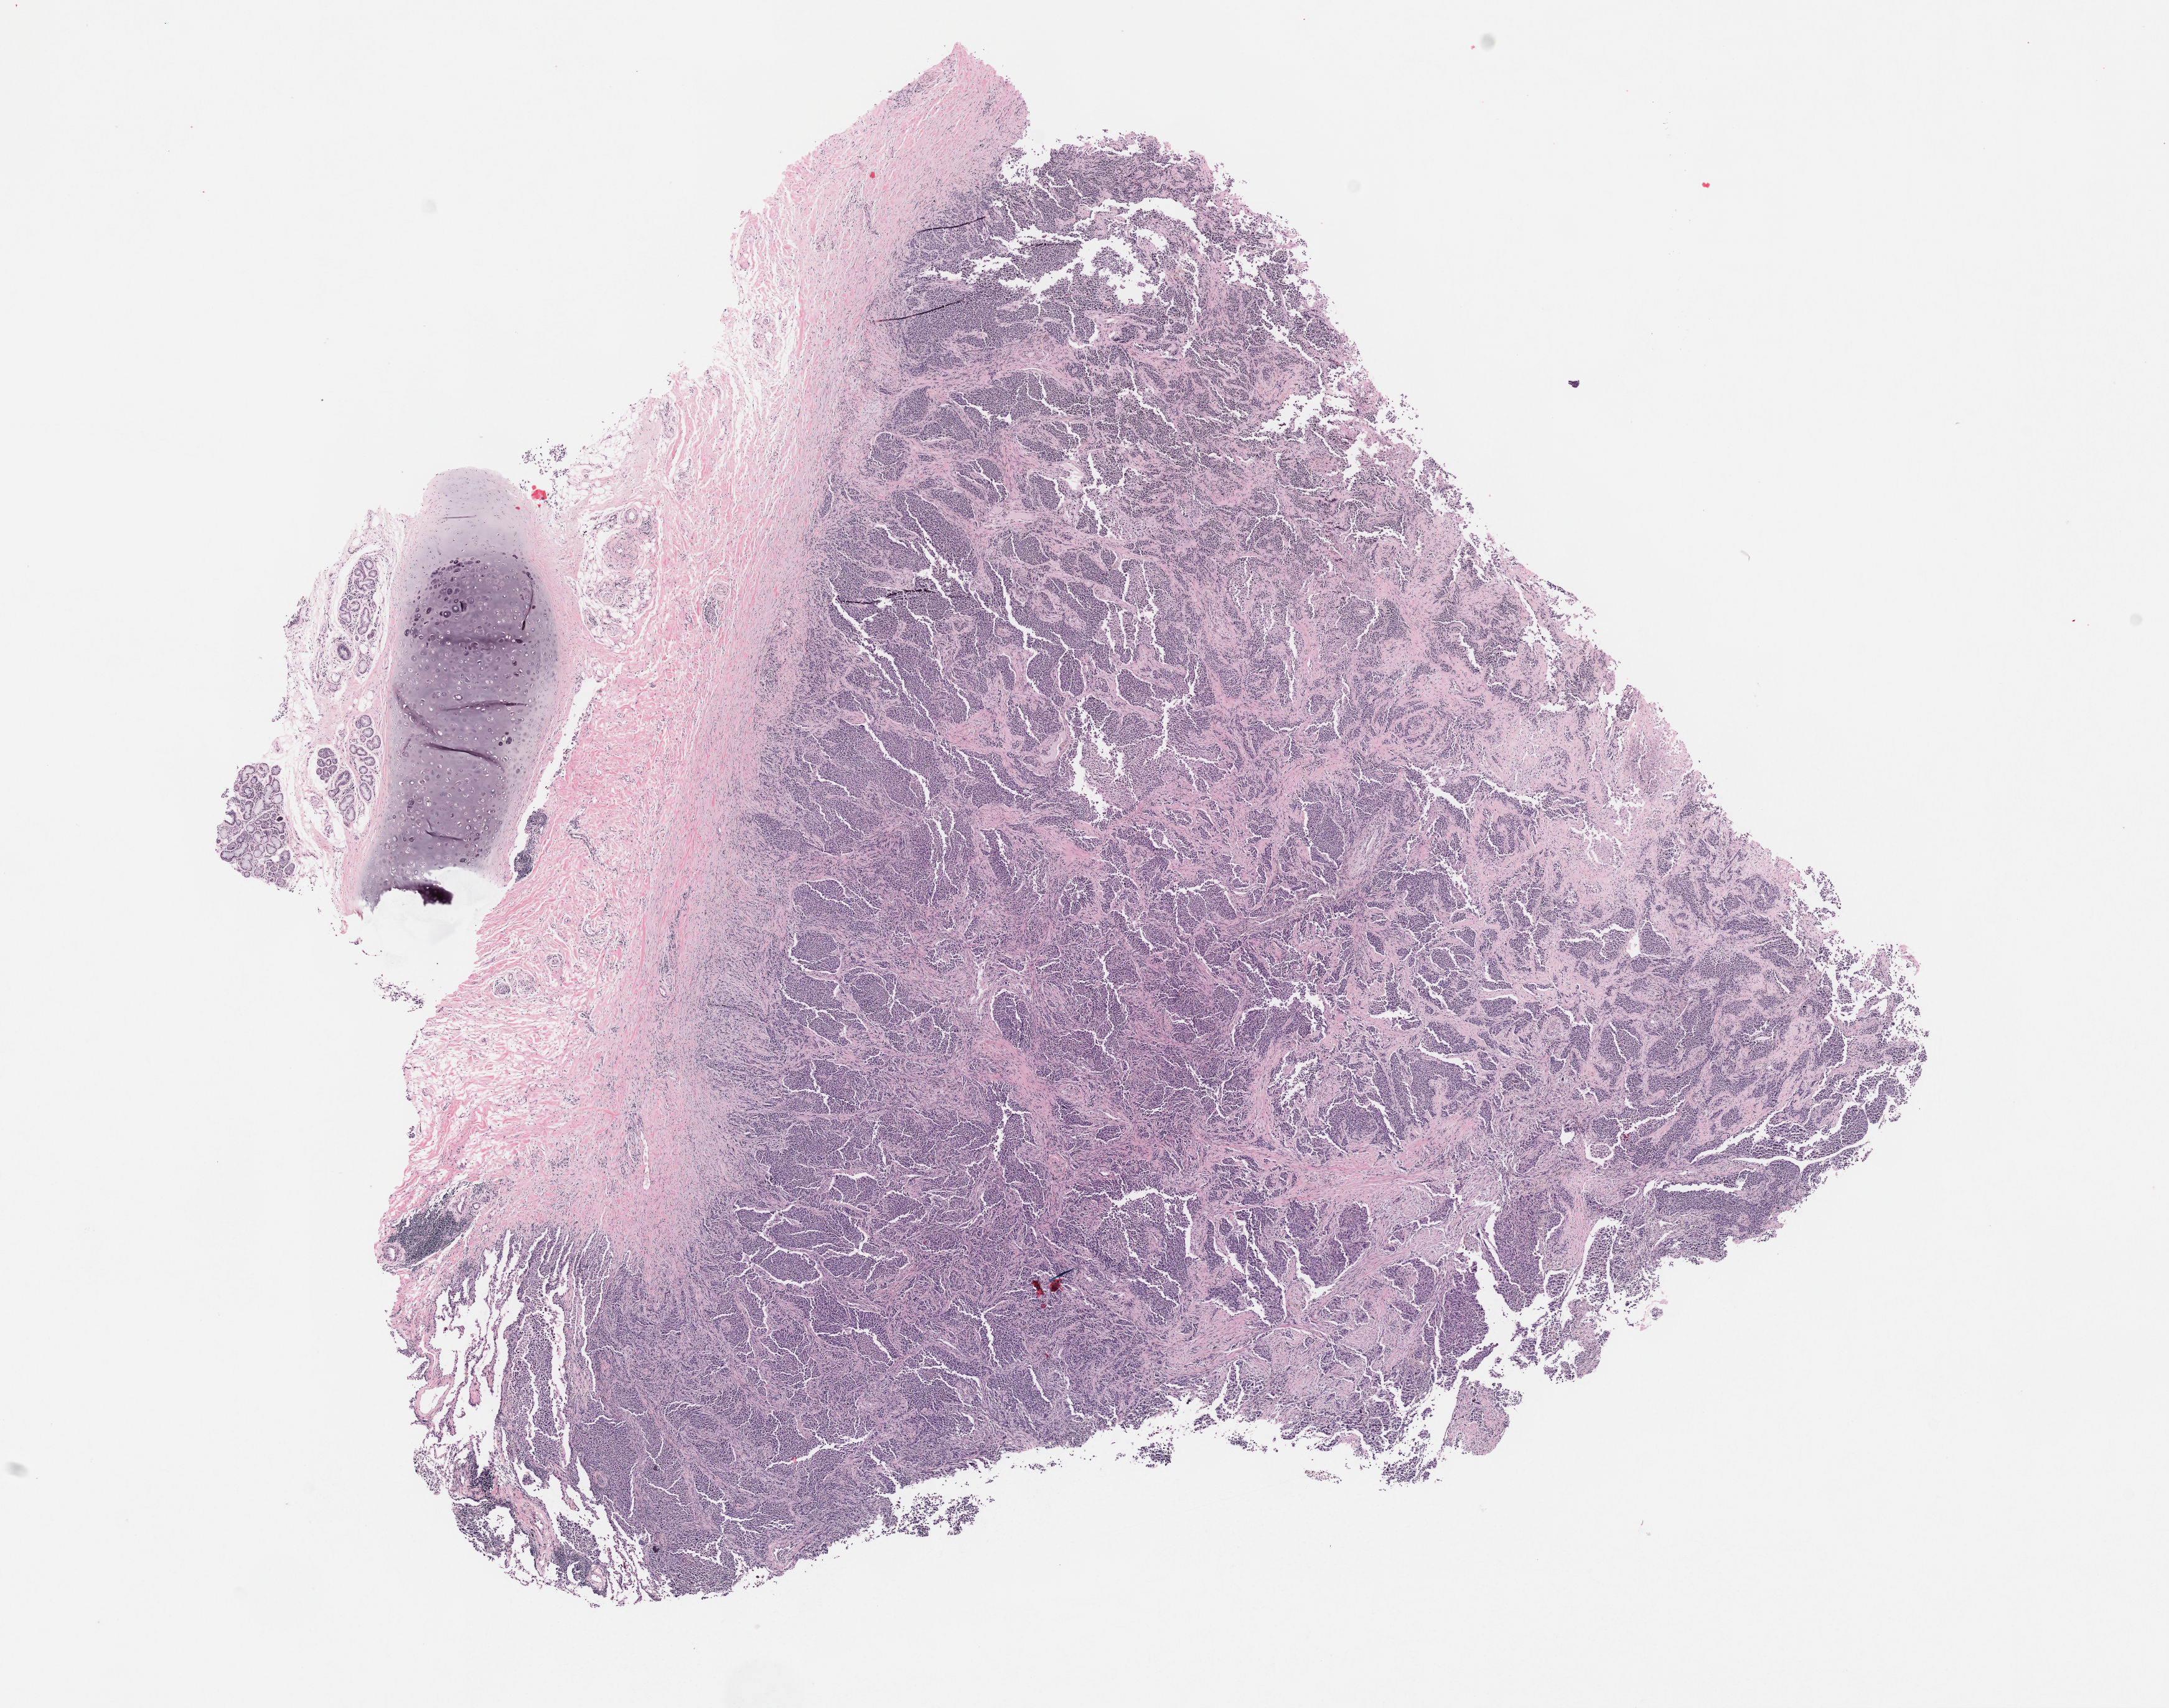
H&E-stained whole-slide image, whole scanned area (about 14.1 x 11.1 mm, acquisition: 40x scan) shown as a low-resolution overview, formalin-fixed paraffin-embedded (FFPE) diagnostic section, primary tumour sample from the lung. Patient: male, age at initial diagnosis 58 years.
Pathologic diagnosis: Adenocarcinoma, NOS (lower lobe, lung). AJCC pathologic stage: IA.